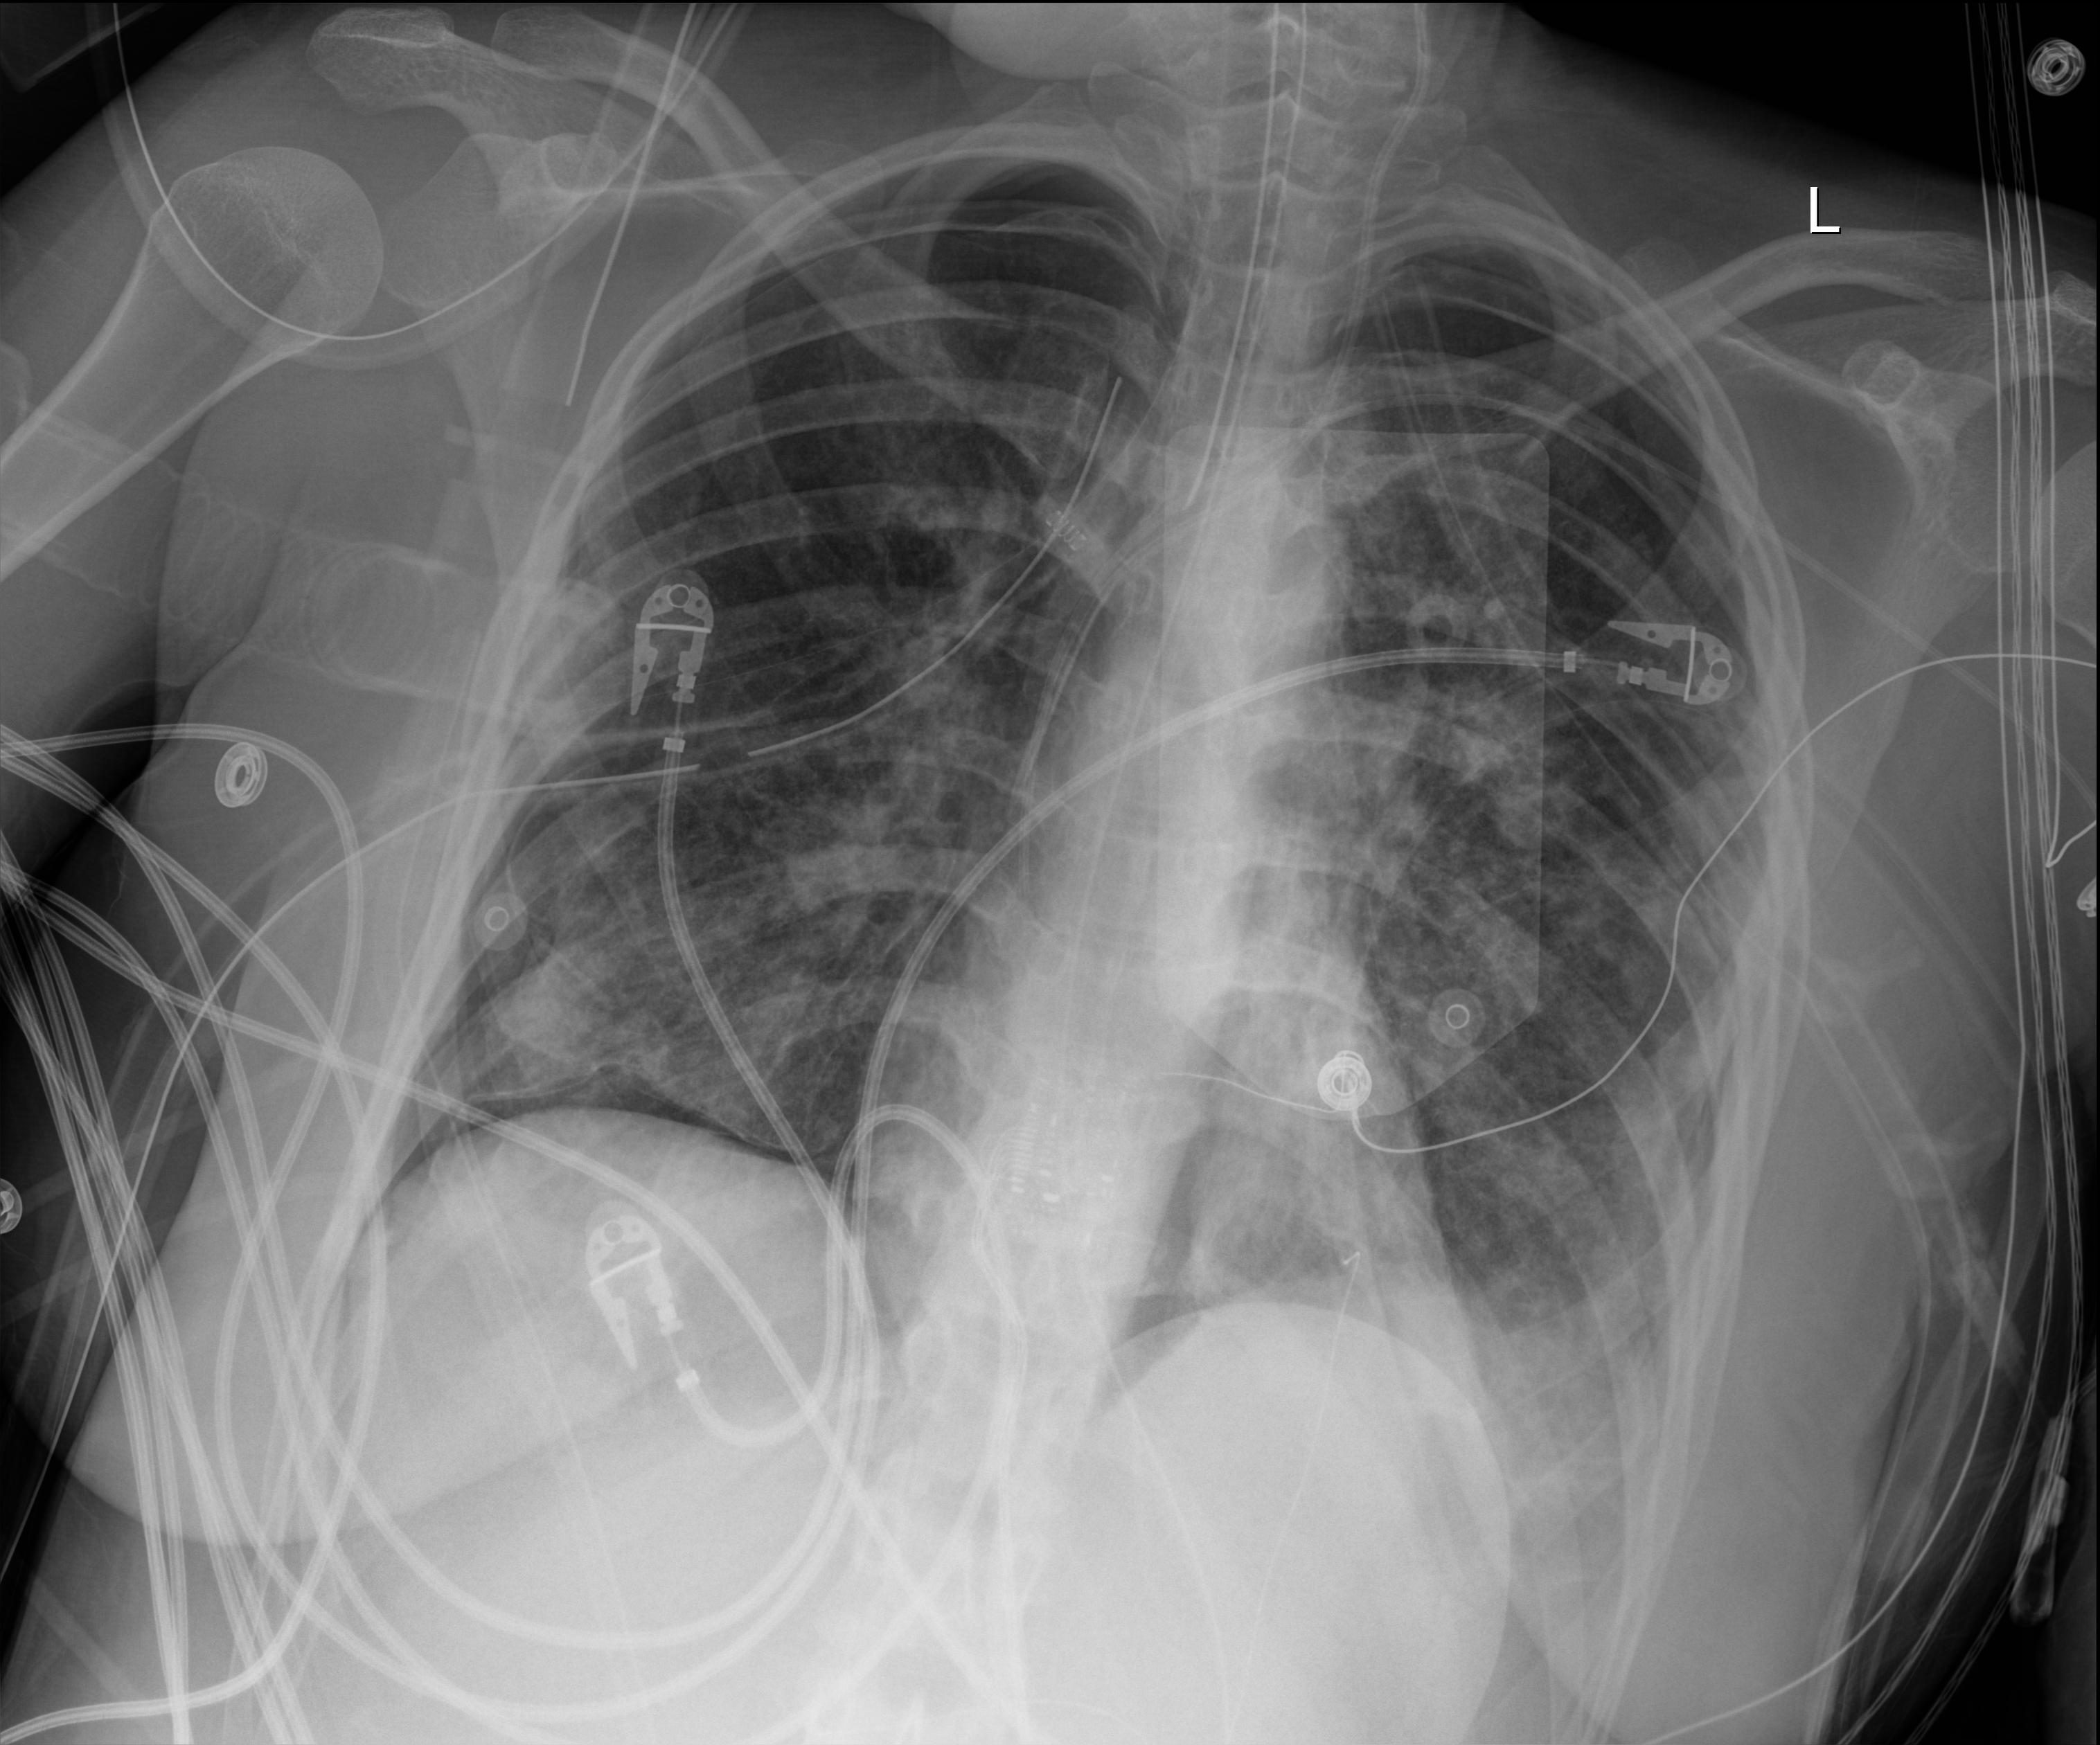
Chest X-ray (portable), anteroposterior (AP) projection. Patient hospitalised with COVID-19, aged 18–59 years.
From the hospital-stay record, not from the radiograph (when in the stay this image was taken is not recorded): admitted to intensive care during this hospital stay: yes; mechanically ventilated during this hospital stay: yes.